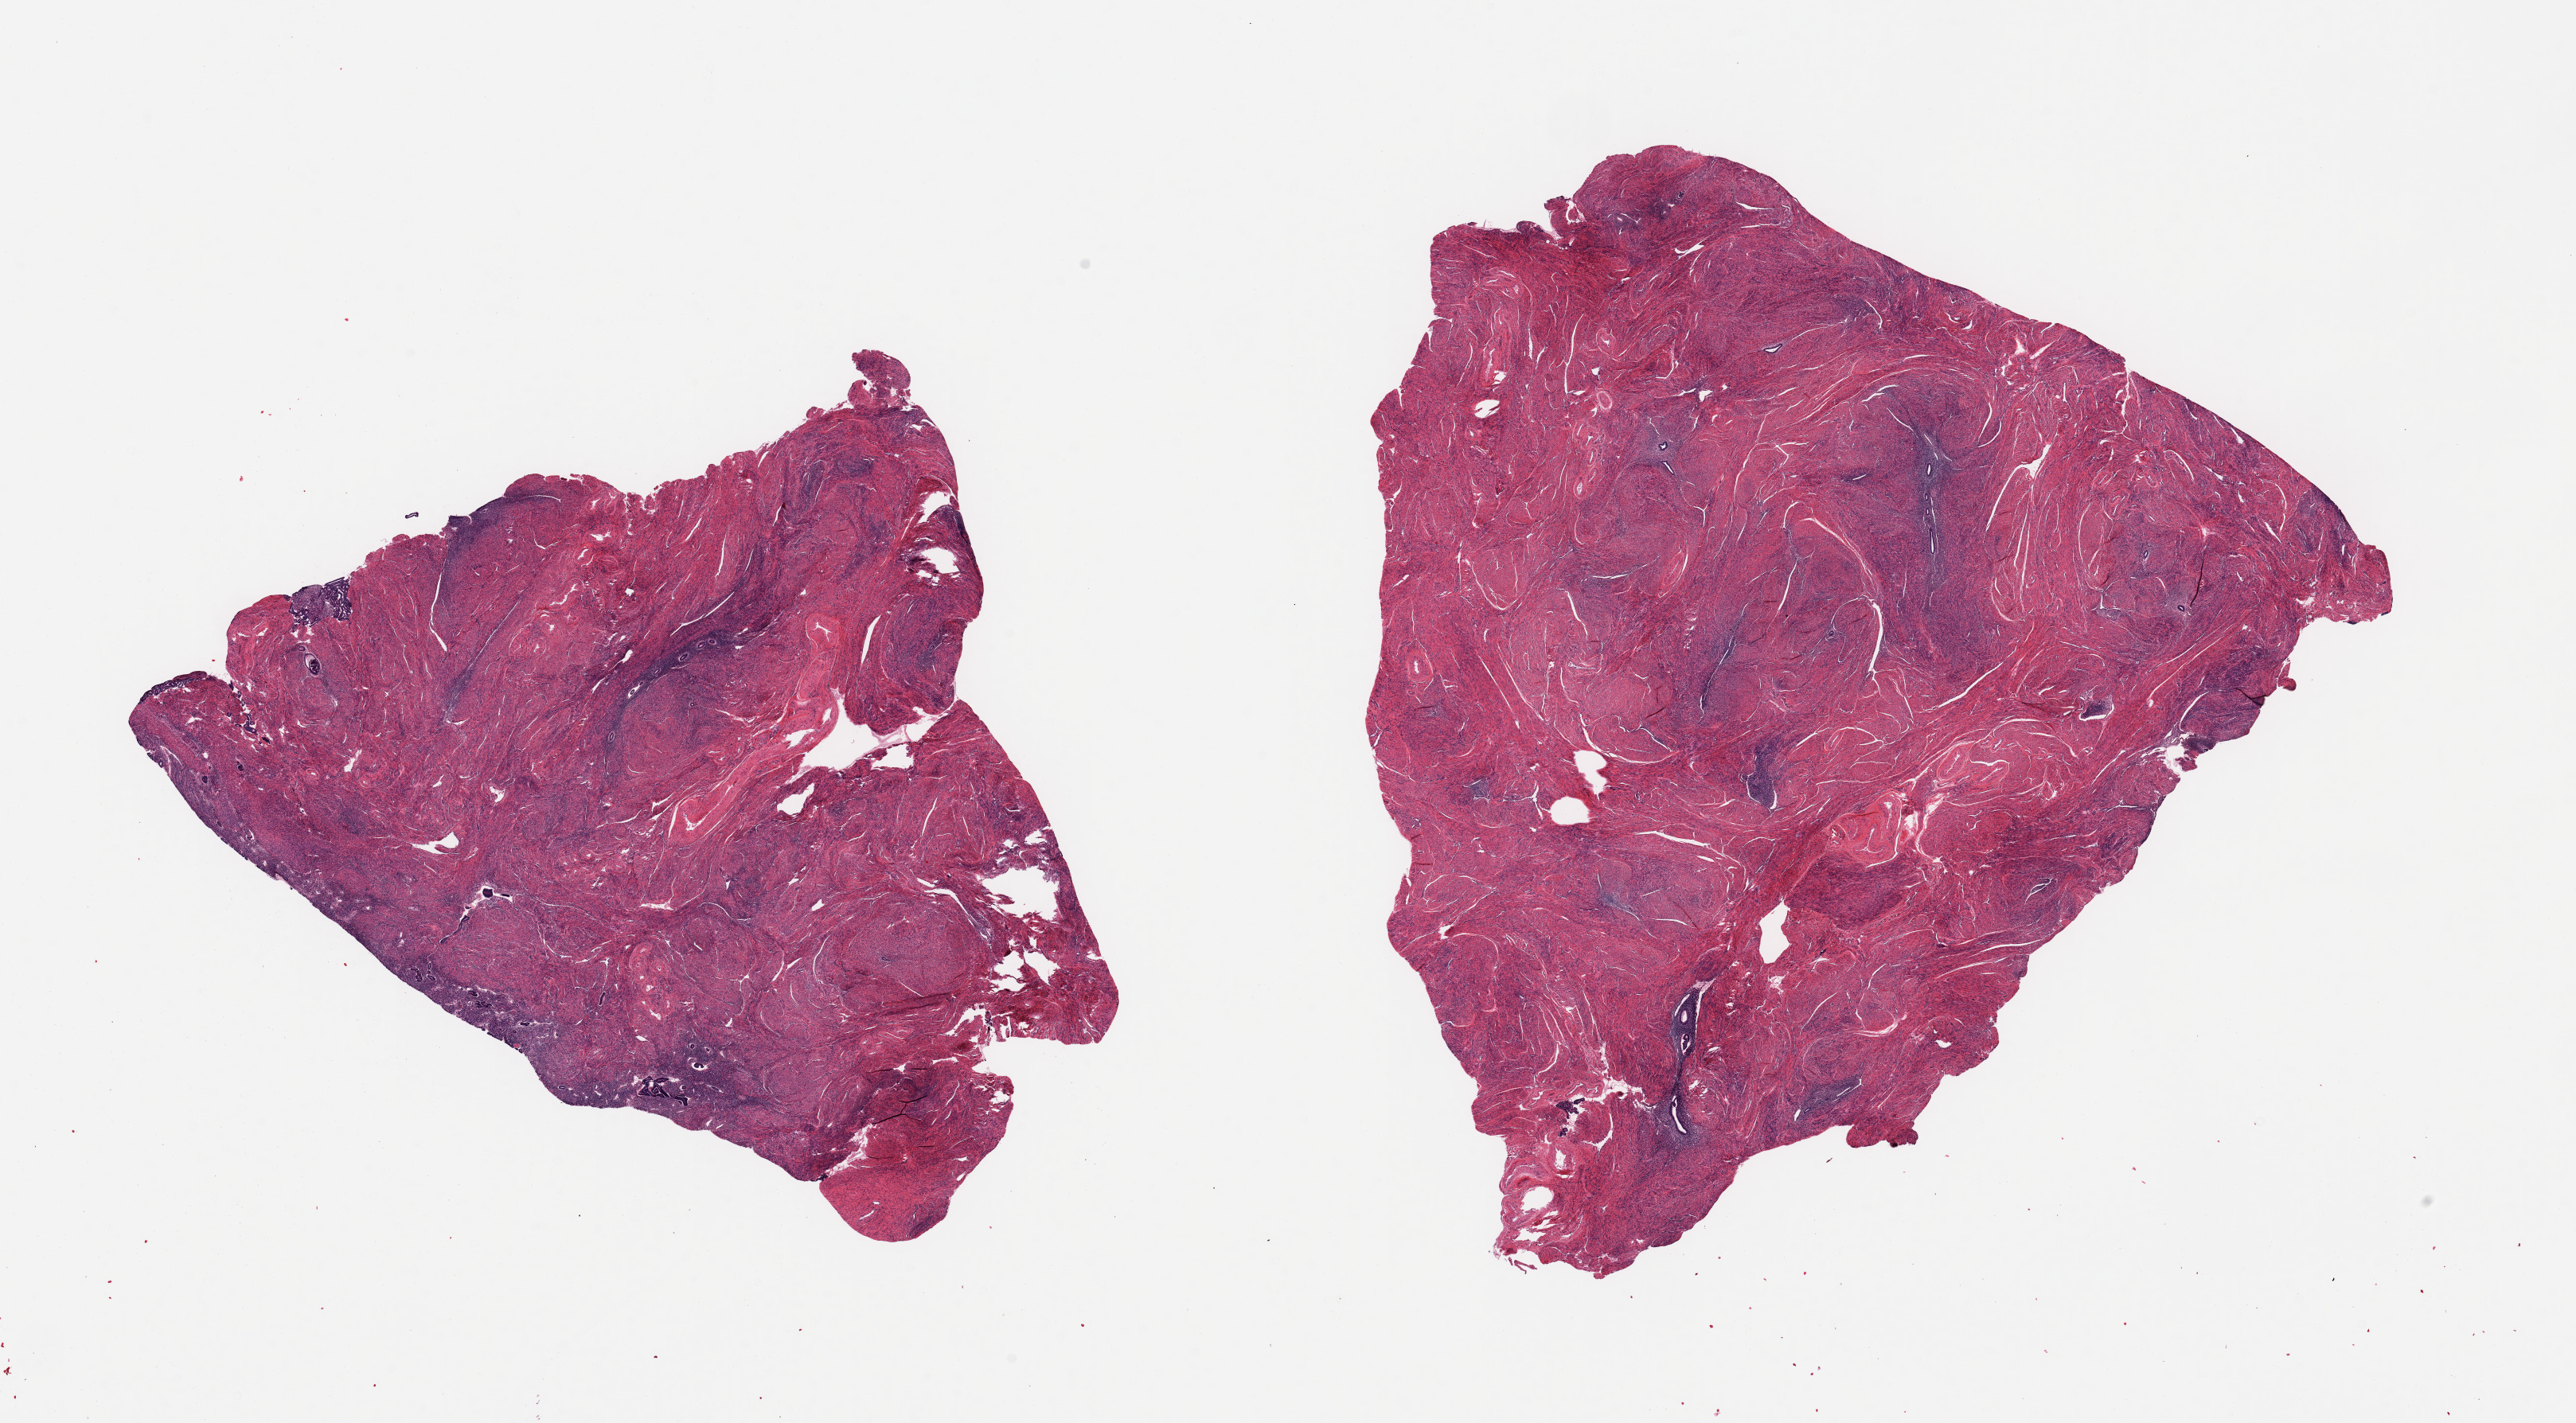
Whole-slide image, H&E stain, brightfield, a low-resolution overview of the entire scanned area, about 25.6 x 14.1 mm (from a 20x scan); PAXgene-fixed paraffin-embedded (PFPE) section; target tissue: uterus; tissue donor sample. Donor: female.
Pathologist's review note for this sample: 2 pieces; moderate adenomyosis; small amount of atrophic endometrium.